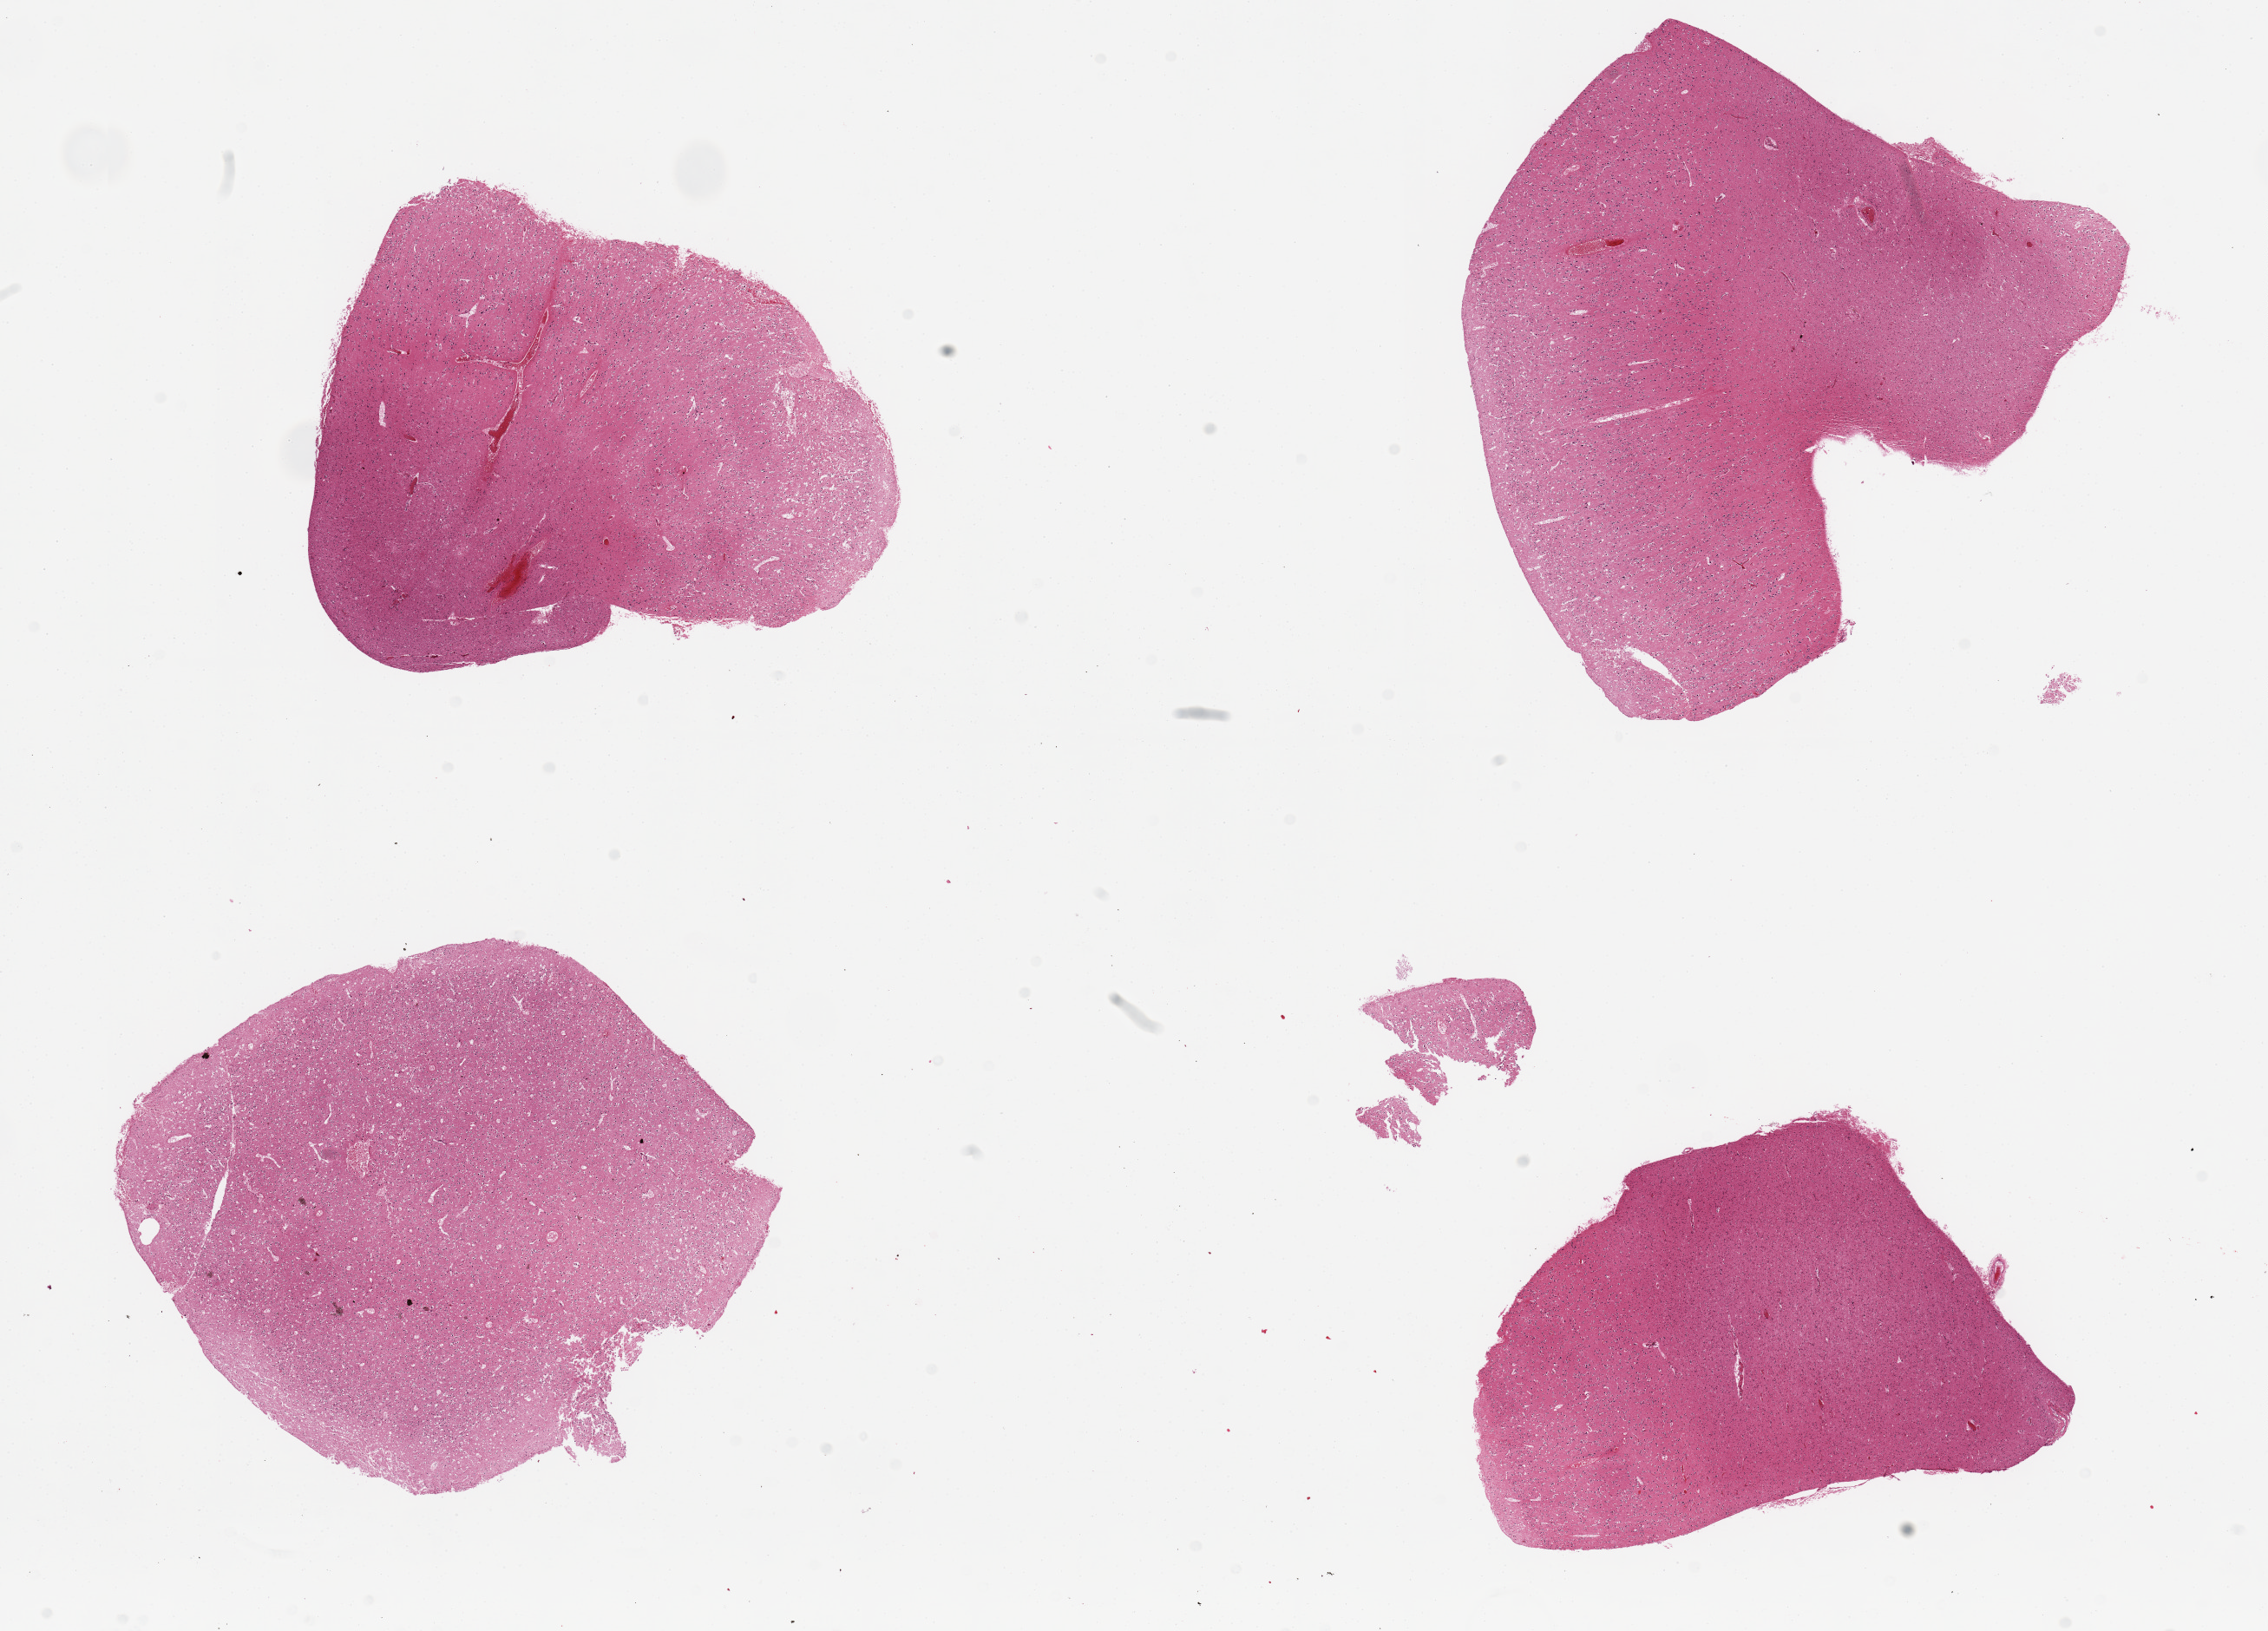
Hematoxylin and eosin (H&E) whole-slide image, brightfield — whole scanned area (about 20.7 x 14.9 mm, acquisition: 20x scan) shown as a low-resolution overview. PAXgene-fixed paraffin-embedded (PFPE) section. Target tissue: cerebral cortex. Donor tissue sample. Donor: male.
Reviewer comment on this tissue sample: 4 pieces.